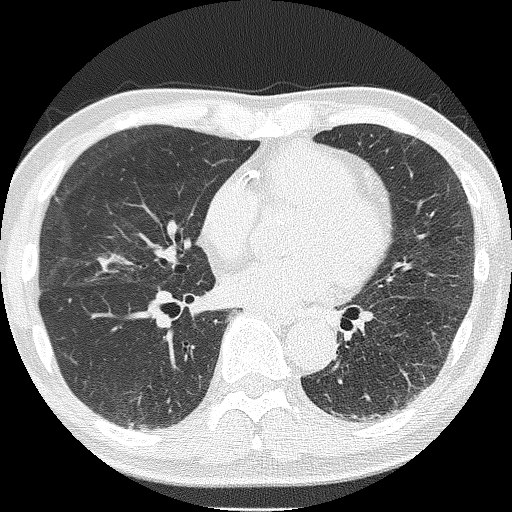
Low-dose screening chest CT, one axial slice. Slice 86 of 181 in the series (ordered by position). Lung window (W 1500 / L -600 HU). 512 × 512 image matrix, field of view 287 × 287 mm.
Annotated regions visible in this slice (outlined manually by an expert reader):
- lesion 1 (tumor, upper lobe of right lung): bounding box (x1, y1, x2, y2) in pixels: (55, 198, 59, 202)